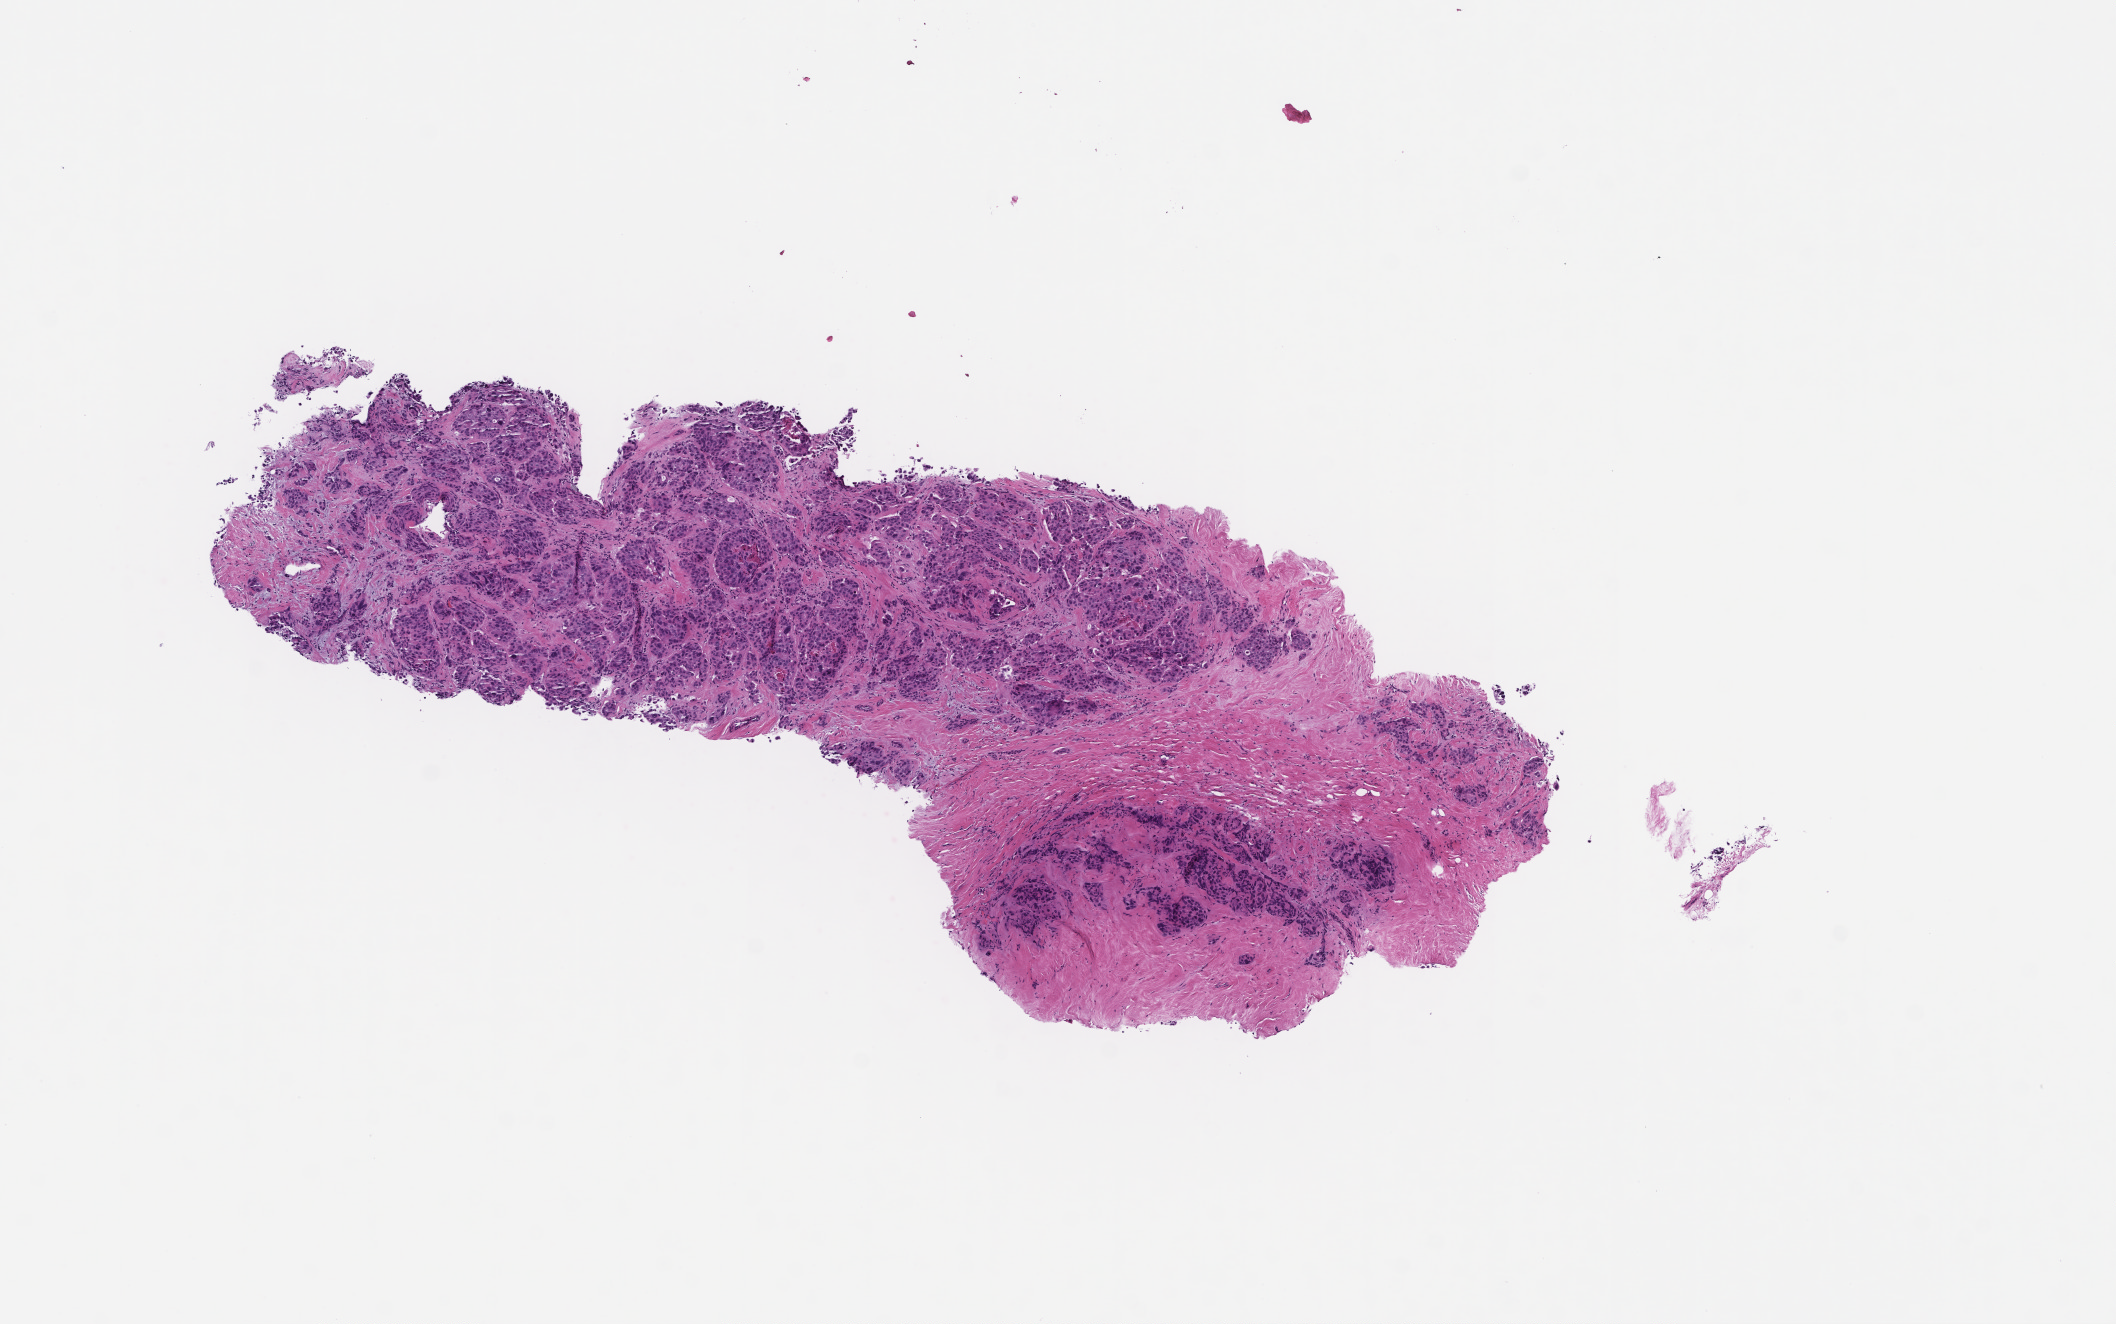
Digitized hematoxylin and eosin (H&E)-stained section — whole scanned area (about 8.5 x 5.3 mm) shown as a low-resolution overview, formalin-fixed paraffin-embedded section, site: breast, collected at baseline (before treatment). Female patient.
This section: primary tumour tissue. Diagnosis: Invasive Breast Carcinoma.